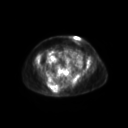
FDG PET of an extremity soft-tissue mass (from a PET/CT study), one axial slice; position 78 of 267 along the scan axis; 3.27 mm slice thickness; 128 × 128 image matrix, field of view 600 × 600 mm. Female patient, age 60 years. From the clinical record (not read from this slice): histological type: spindle cell suggestive of myxofibrosarcoma; grade: intermediate; site of the primary tumour: right buttock.
Structures marked on this image (expert contour drawn on MRI and transferred to this co-registered scan by the dataset authors):
- gross tumour volume (mass): box from (x=47, y=84) to (x=62, y=93) px